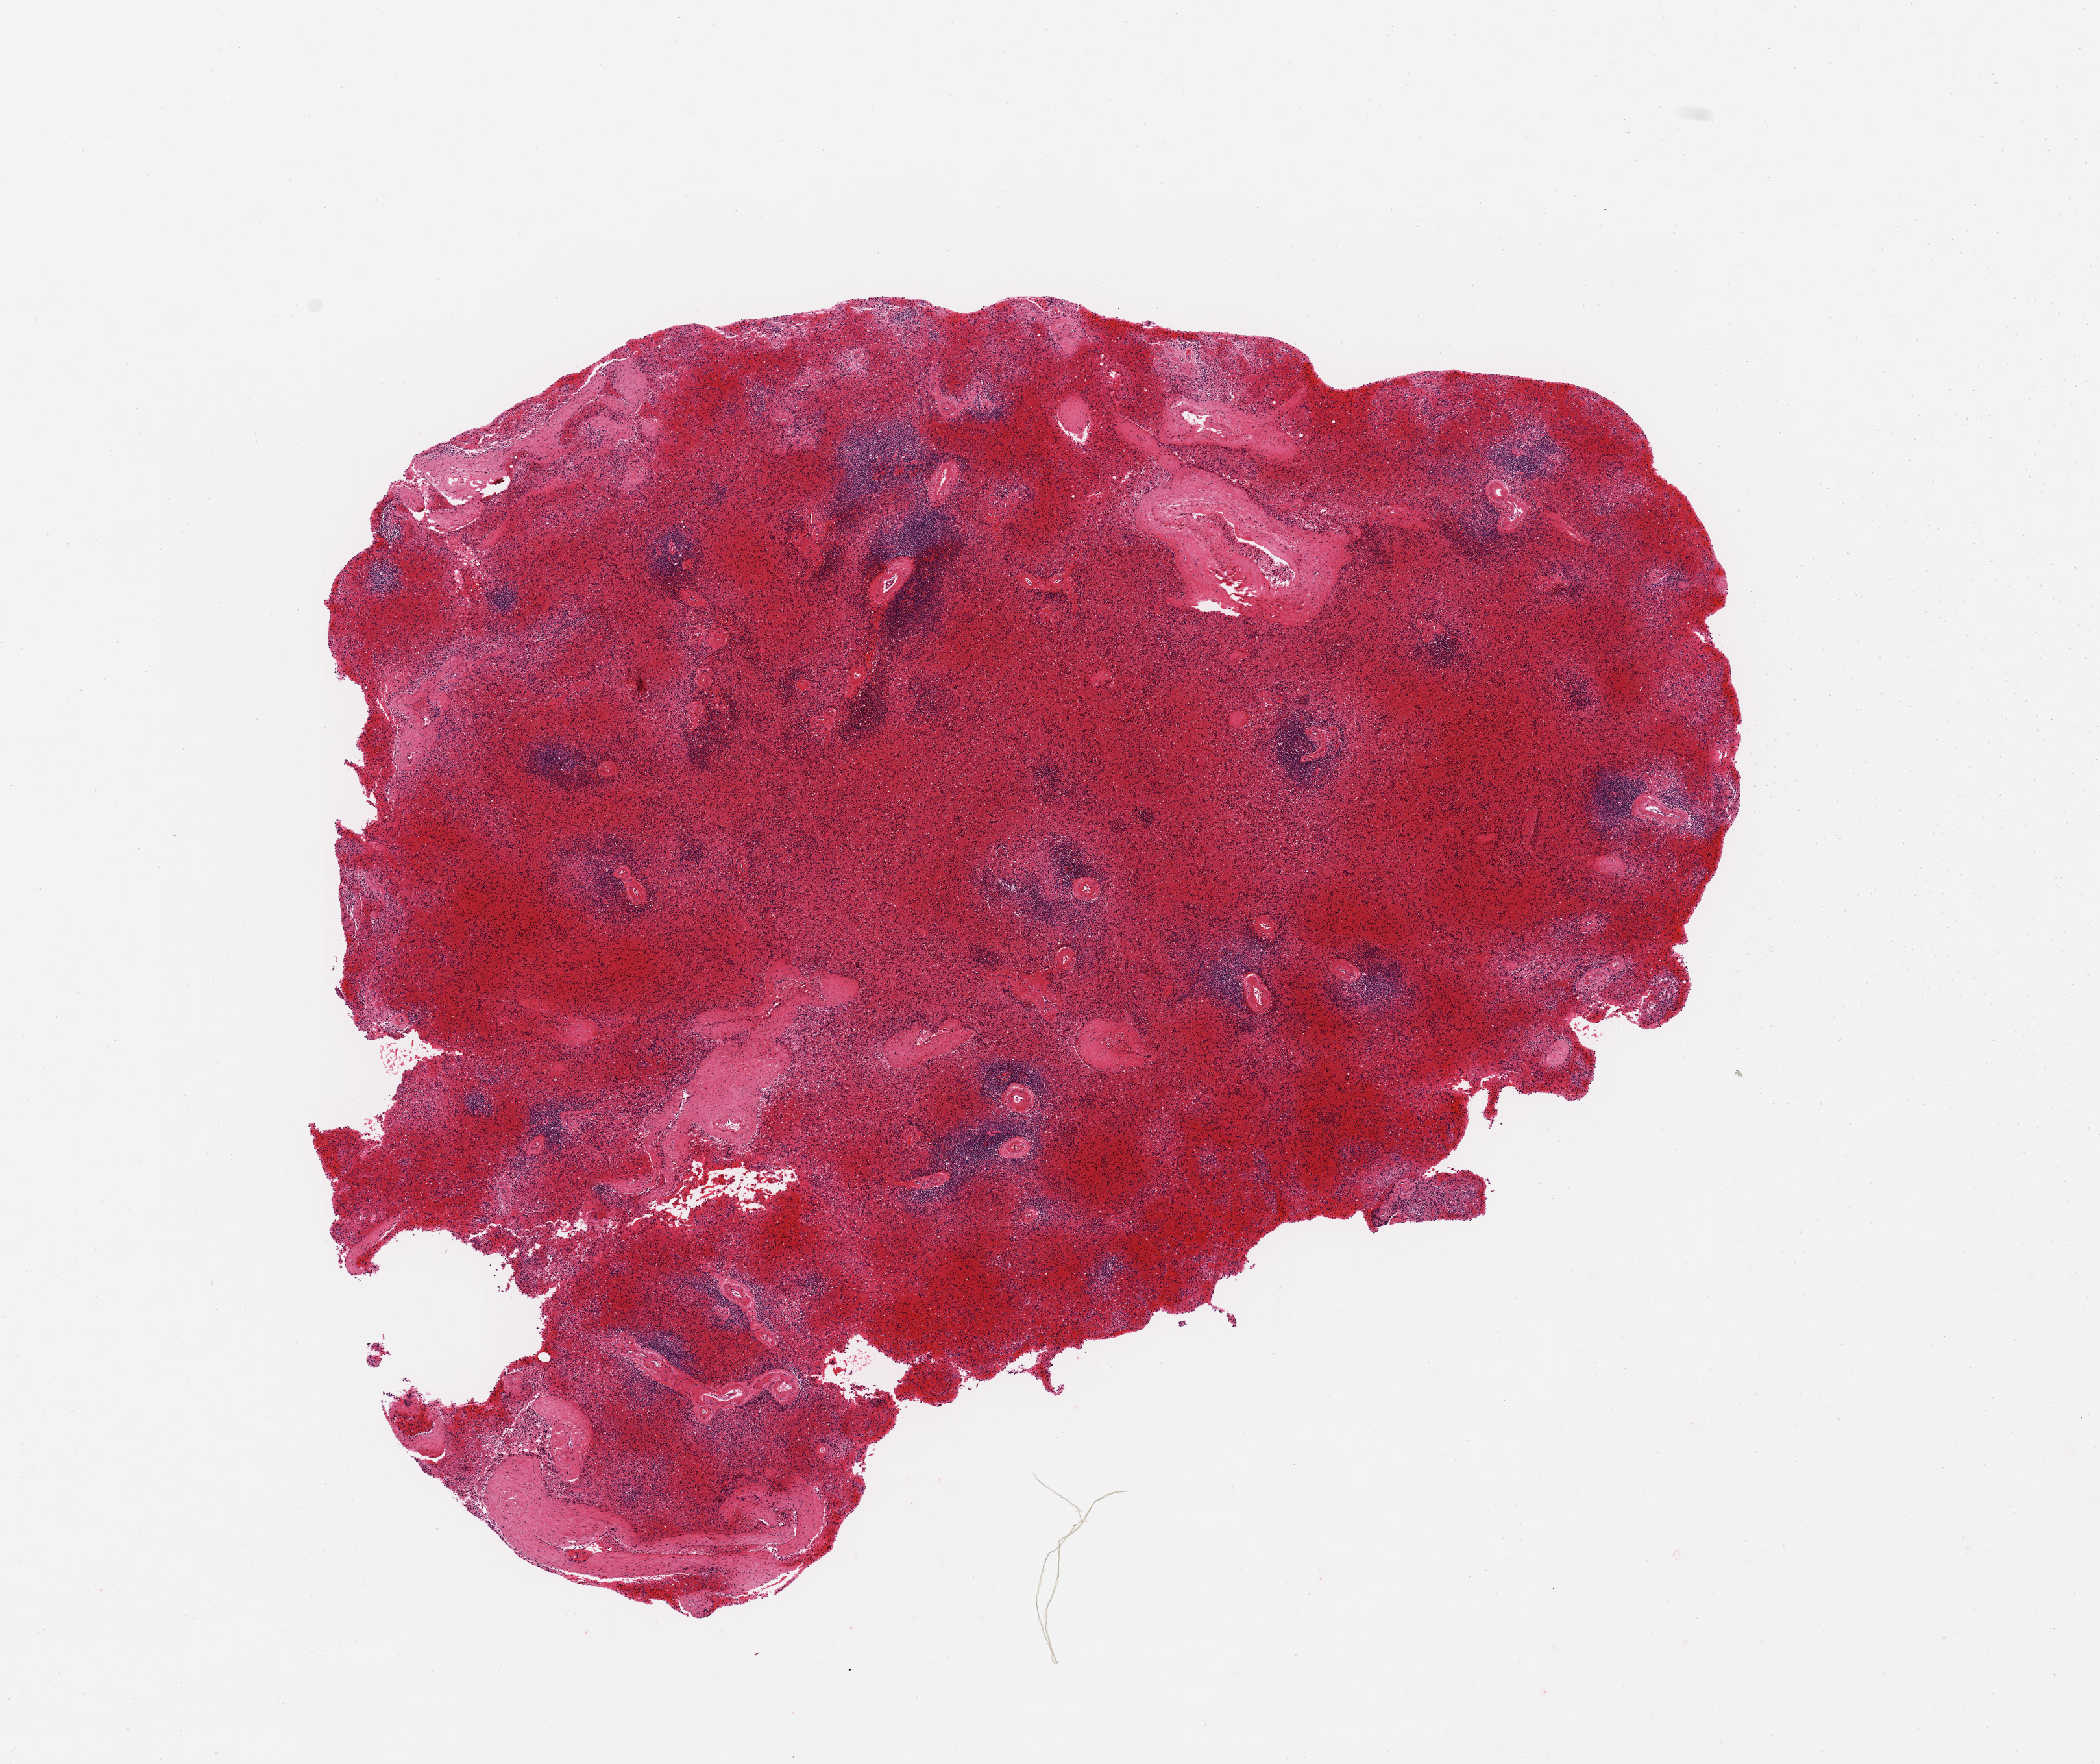
Whole-slide image, haematoxylin and eosin stain — whole scanned area (about 12.8 x 10.7 mm) shown as a low-resolution overview, PAXgene-fixed paraffin-embedded (PFPE) section, section of spleen (target tissue), tissue donor sample. Donor: female.
* pathologist's review note for this sample: 8.5x6.7mm. Areas of poor/under fixation